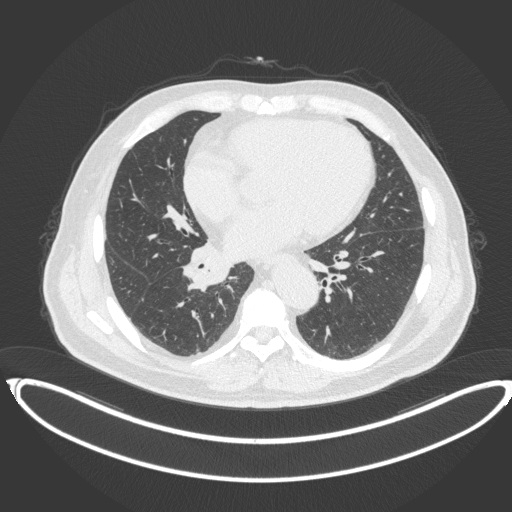
Chest CT, one axial slice. Position 177 of 383 along the scan axis. Reconstruction kernel B31f. 120 kVp. Lung window (W 1500 / L -600 HU). 512 × 512 image matrix, field of view 448 × 448 mm. Patient: male, 61 years. Case-level facts recorded for this patient, not image findings: clinical TNM (as recorded): T1b N1 M0.
Outlined on this slice (rectangle marked by the reading radiologist):
- lung tumour (recorded histology: squamous cell carcinoma): box from (x=178, y=240) to (x=230, y=292) px